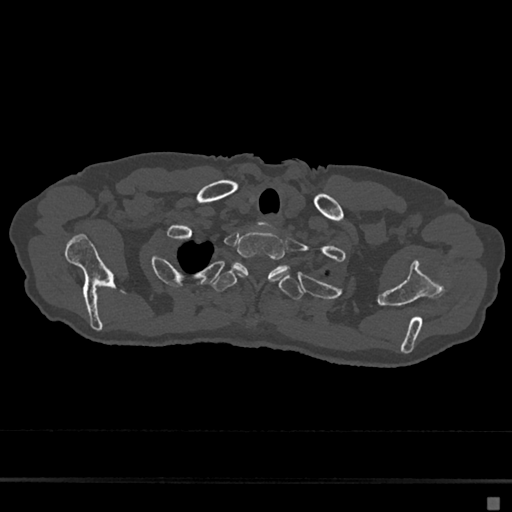
CT including the spine, one axial slice; slice 594 of 797 in the series (ordered by position); 120 kVp; bone window (W 1800 / L 400 HU); 512 × 512 image matrix. Female patient, age 68 years. From the clinical record (not read from this slice): primary cancer: renal.
Annotated regions visible in this slice (semi-automatically segmented with operator editing):
- T1 vertebra: bounding box (x1, y1, x2, y2) in pixels: (236, 231, 290, 281)
- T2 vertebra: (211, 262, 304, 300)